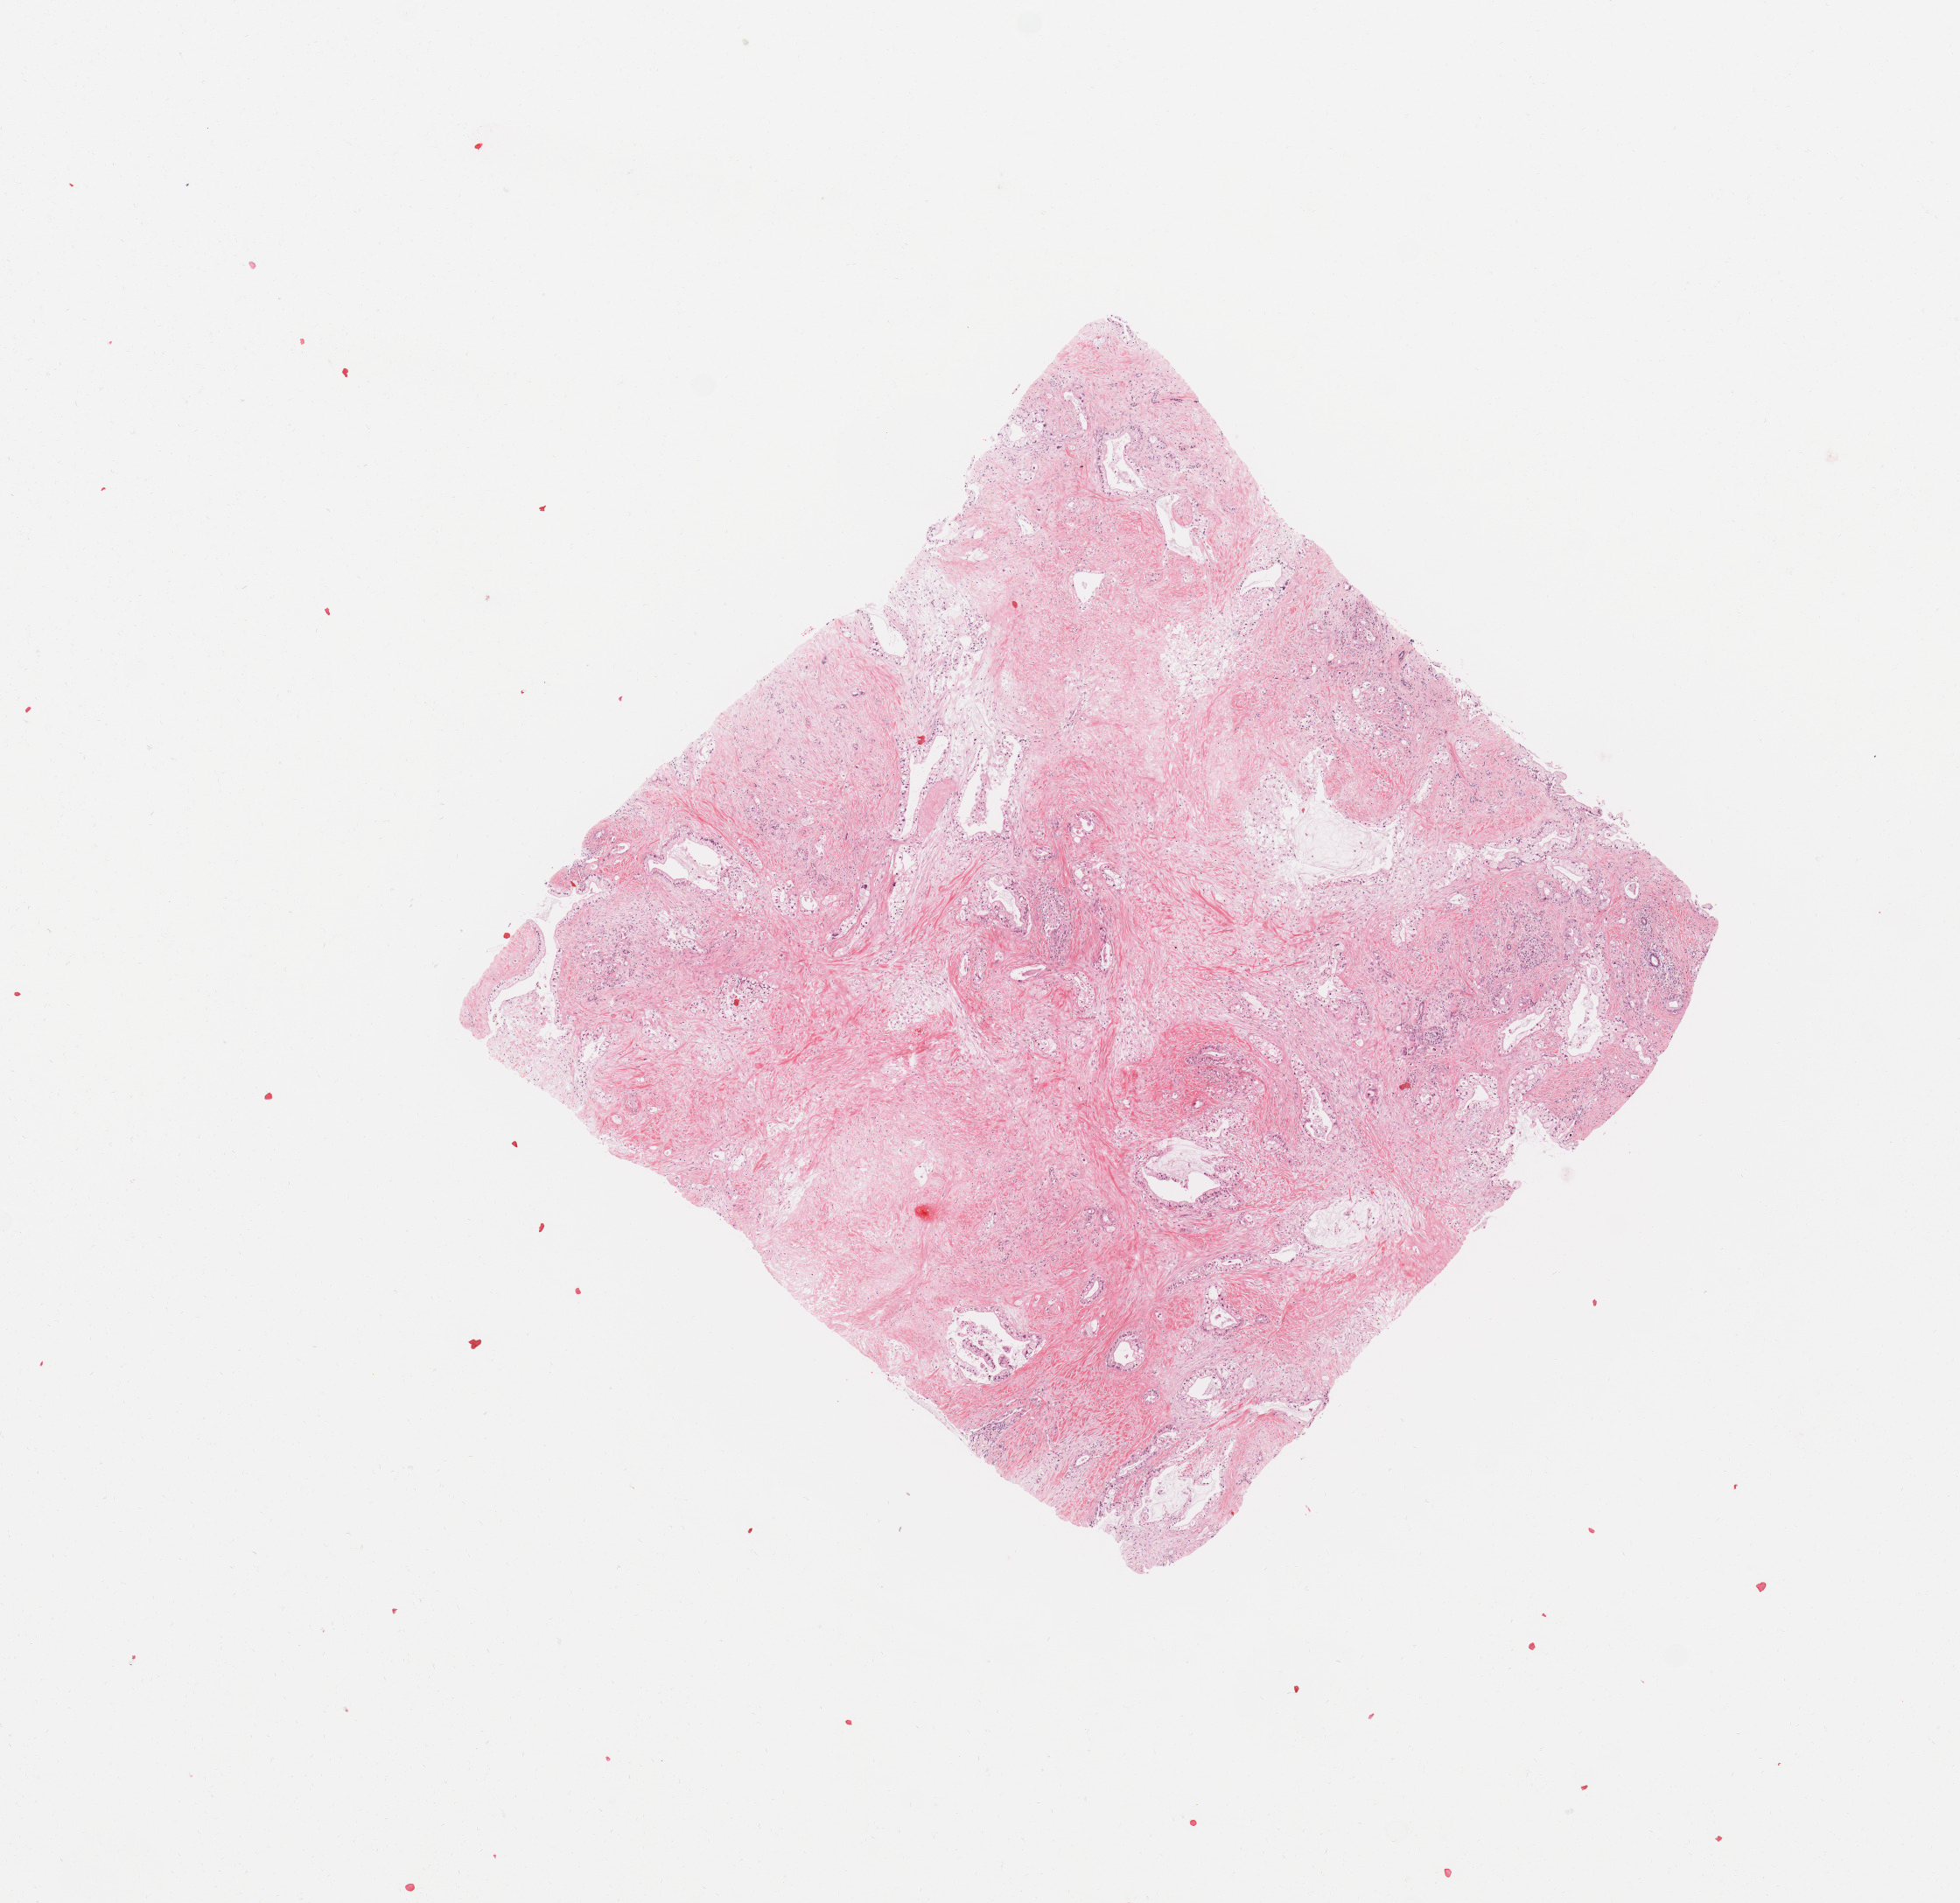
H&E-stained whole-slide image, a low-resolution overview of the entire scanned area, about 8.9 x 8.6 mm; tumour tissue sample, sampled site: pancreas. Patient: female, age 41 years. Histologic grade: G2 (moderately differentiated). Pathologist review of this section (percent, as recorded): tumour nuclei 30%, necrosis 0%.
Histologic diagnosis: Infiltrating duct carcinoma, NOS. AJCC pathologic stage: III.